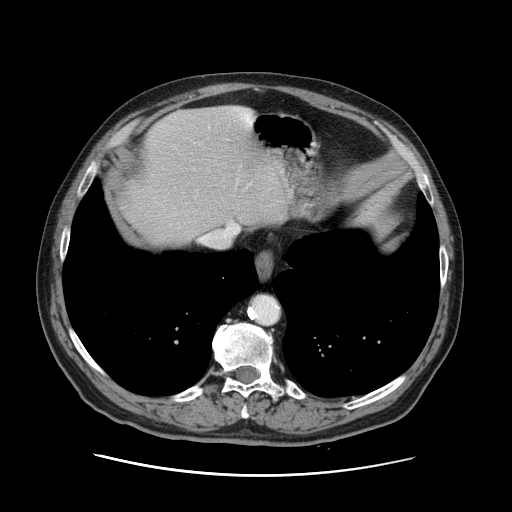
Contrast-enhanced abdominal CT, one axial slice. Slice 112 of 141 in the series (ordered by position). 120 kVp. Intravenous contrast given. Soft-tissue window (W 400 / L 40 HU). 512 × 512 image matrix. Male patient, age 72 years. From the clinical record (not read from this slice): diagnosis: colorectal cancer liver metastases, imaged before liver resection; multiple liver metastases: yes; largest metastasis: 5.4 cm; chemotherapy before resection: yes.
Outlined on this slice (expert manual segmentation):
- hepatic veins: bounding box (x1, y1, x2, y2) in pixels: (224, 183, 251, 235)
- liver: (119, 106, 284, 245)
- planned liver remnant (the part of the liver to remain after resection): (149, 106, 283, 245)
- portal vein (with intrahepatic branches): (228, 227, 235, 235)